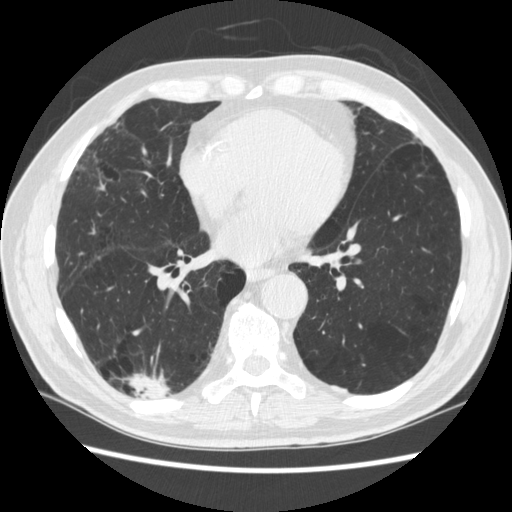
Low-dose screening chest CT, one axial slice. Position 116 of 266 along the scan axis. 120 kVp. Lung window (W 1500 / L -600 HU). 1.25 mm slice thickness. 512 × 512 image matrix.
Structures marked on this image (outlined manually by an expert reader):
- lesion 1 (tumor, upper lobe of right lung): bounding box (x1, y1, x2, y2) in pixels: (130, 375, 169, 399)